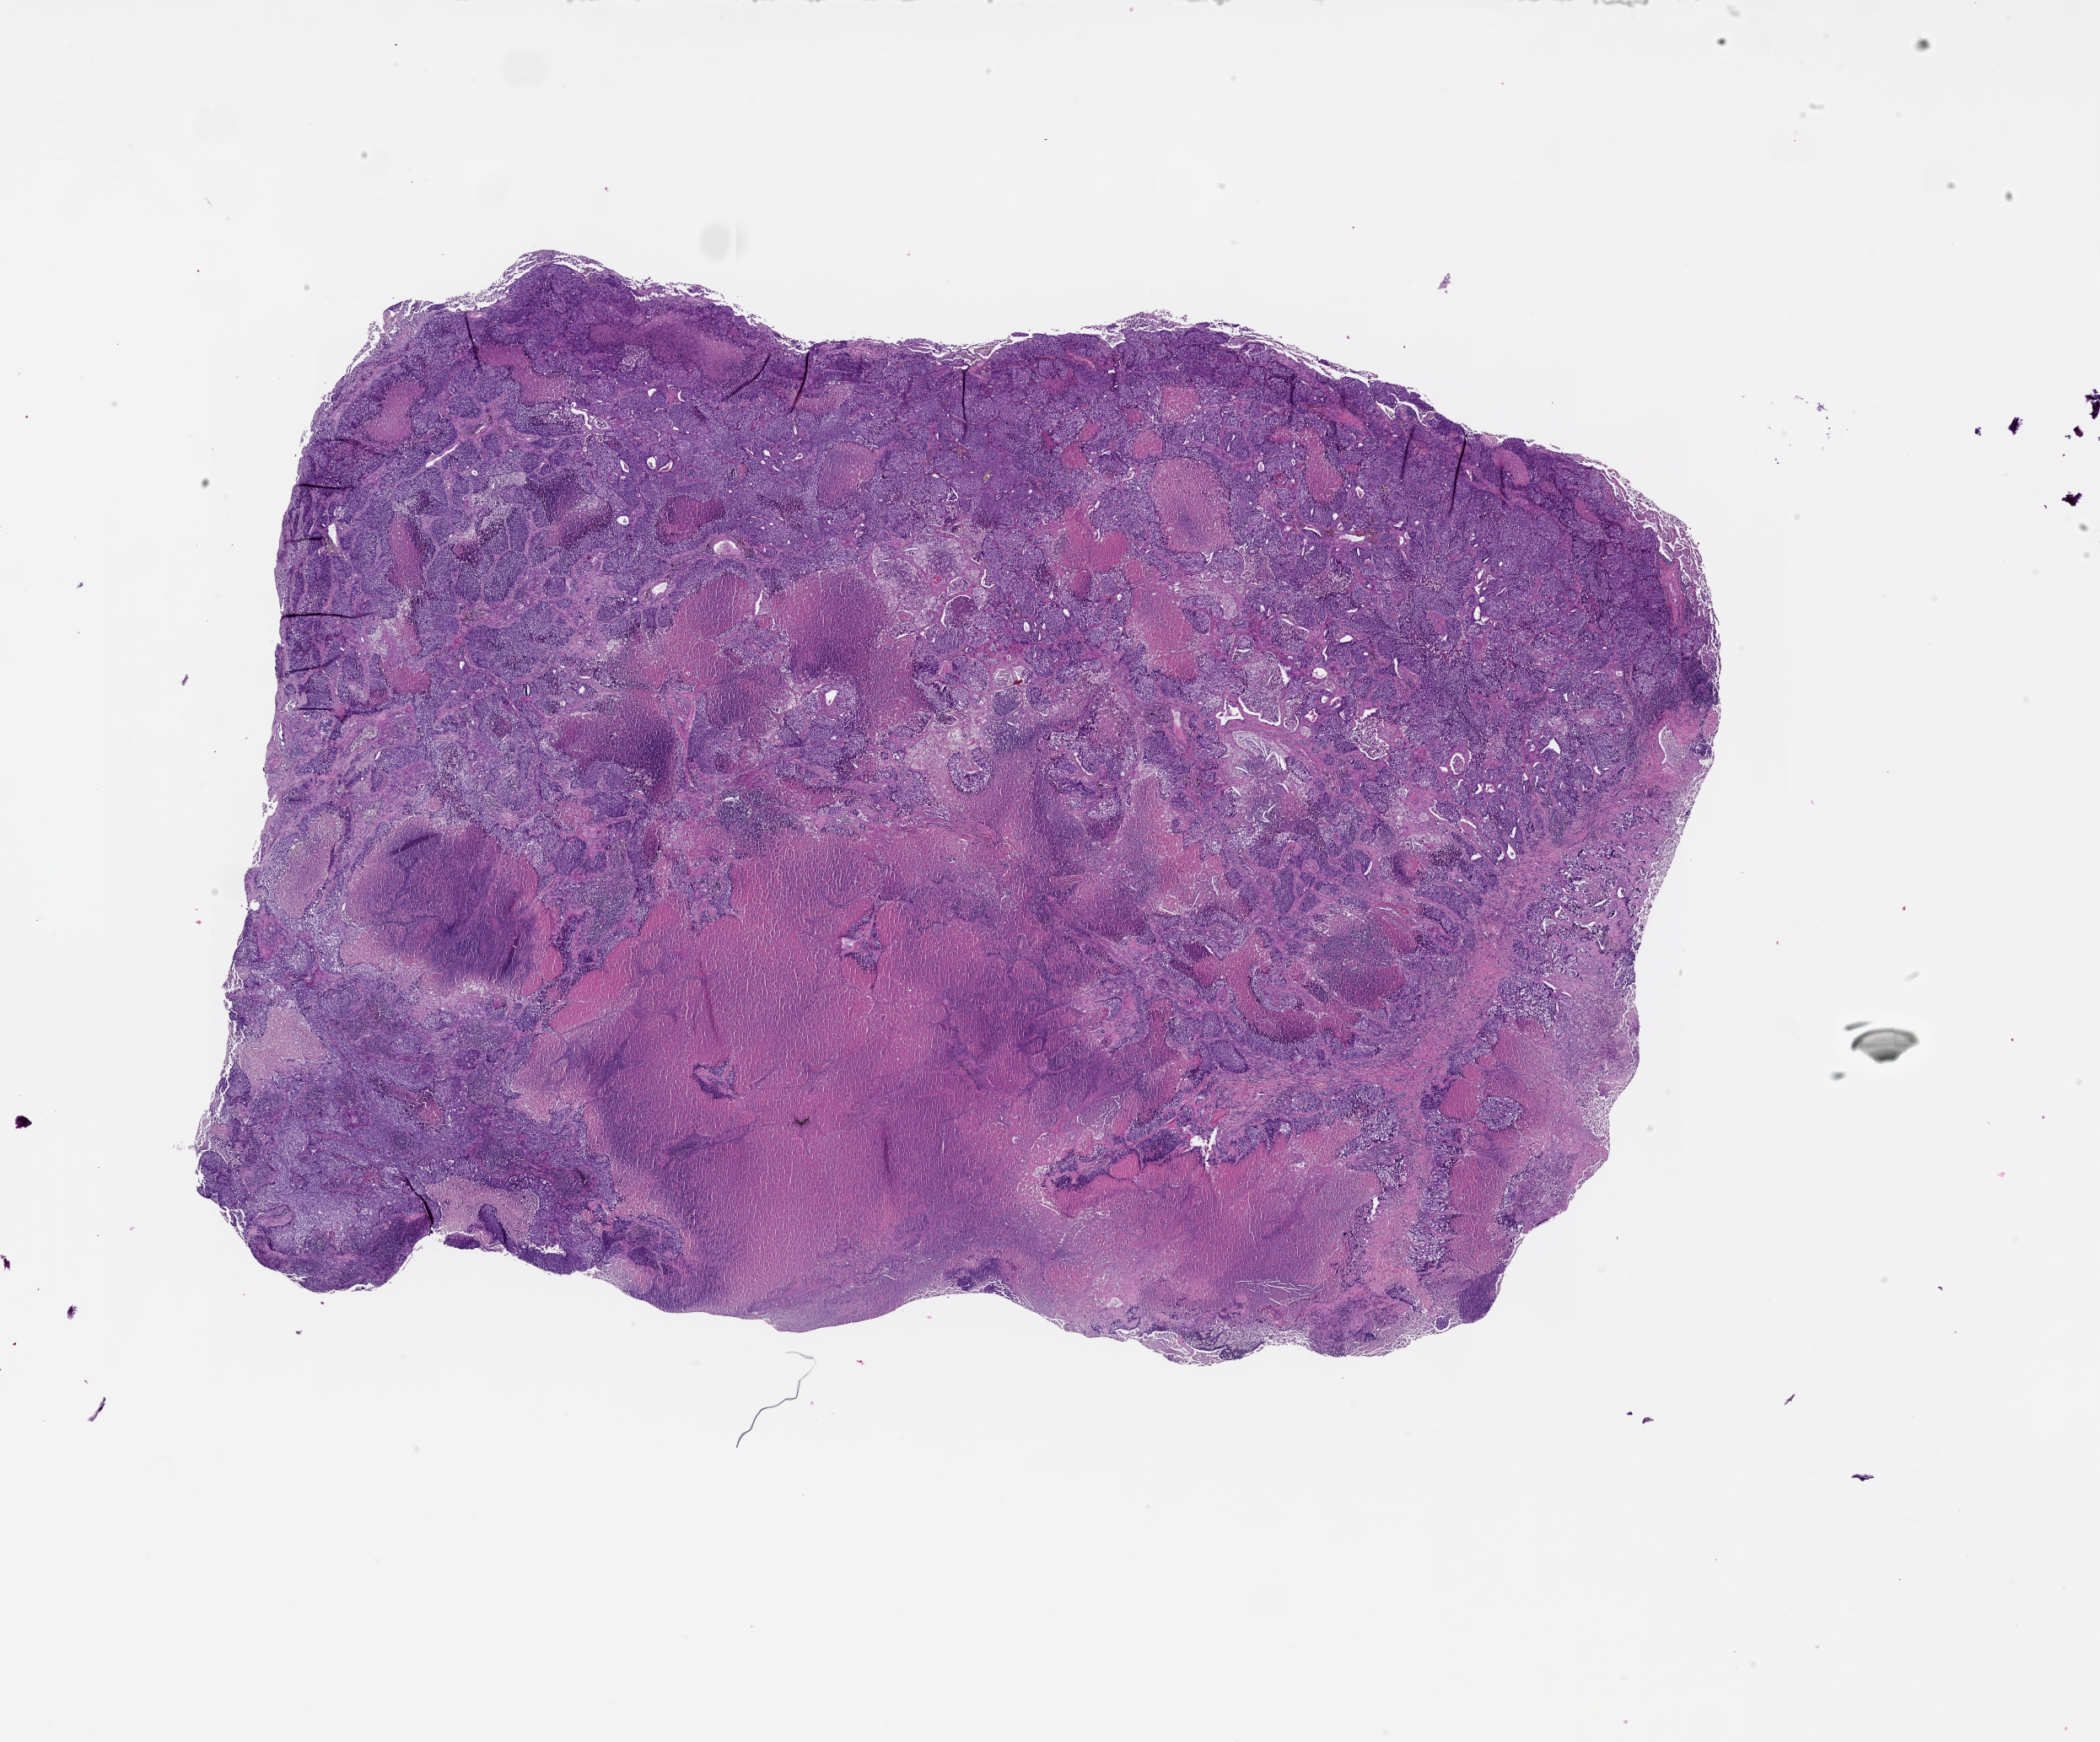
Digitized Hematoxylin and eosin (H&E) stained tissue section (whole slide), whole scanned area (about 20.0 x 16.6 mm, slide scanned at 20x) shown as a low-resolution overview; tumour tissue sample, lung. Male, 54 y/o.
Patient diagnosis (cohort enrolment): squamous cell carcinoma (lung).